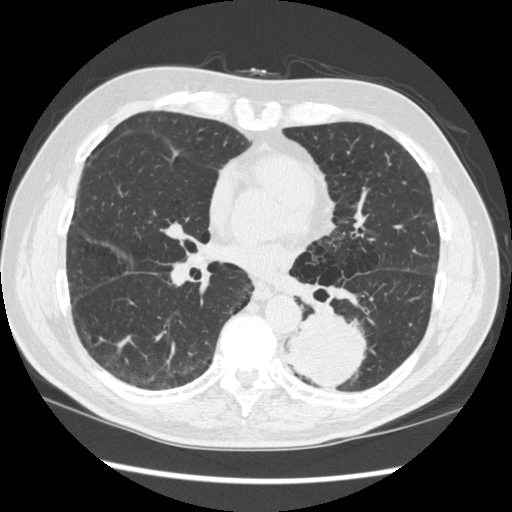
Chest CT (low-dose screening protocol), one axial image. Baseline screening round. Lung window (W 1500 / L -600 HU). Standard (soft-tissue) reconstruction kernel (STANDARD). 120 kVp. Male participant, aged 72 years at enrolment. Current smoker at enrolment.
Expert-annotated lung lesion, bounding box (x1, y1, x2, y2) in pixels: (267, 303, 371, 395). The screening reader recorded 2 non-calcified nodules or masses ≥4 mm on this exam (left lower lobe, right middle lobe); which of them this box marks is not recorded. Official screen result: positive, change unspecified: nodule(s) >= 4 mm or enlarging nodule(s), mass(es), or other non-specific abnormalities suspicious for lung cancer. Participant outcome: lung cancer diagnosed 37 days after this screen — squamous cell carcinoma, NOS, left lower lobe, stage IIIA (AJCC 6th edition), 60 mm at pathology.